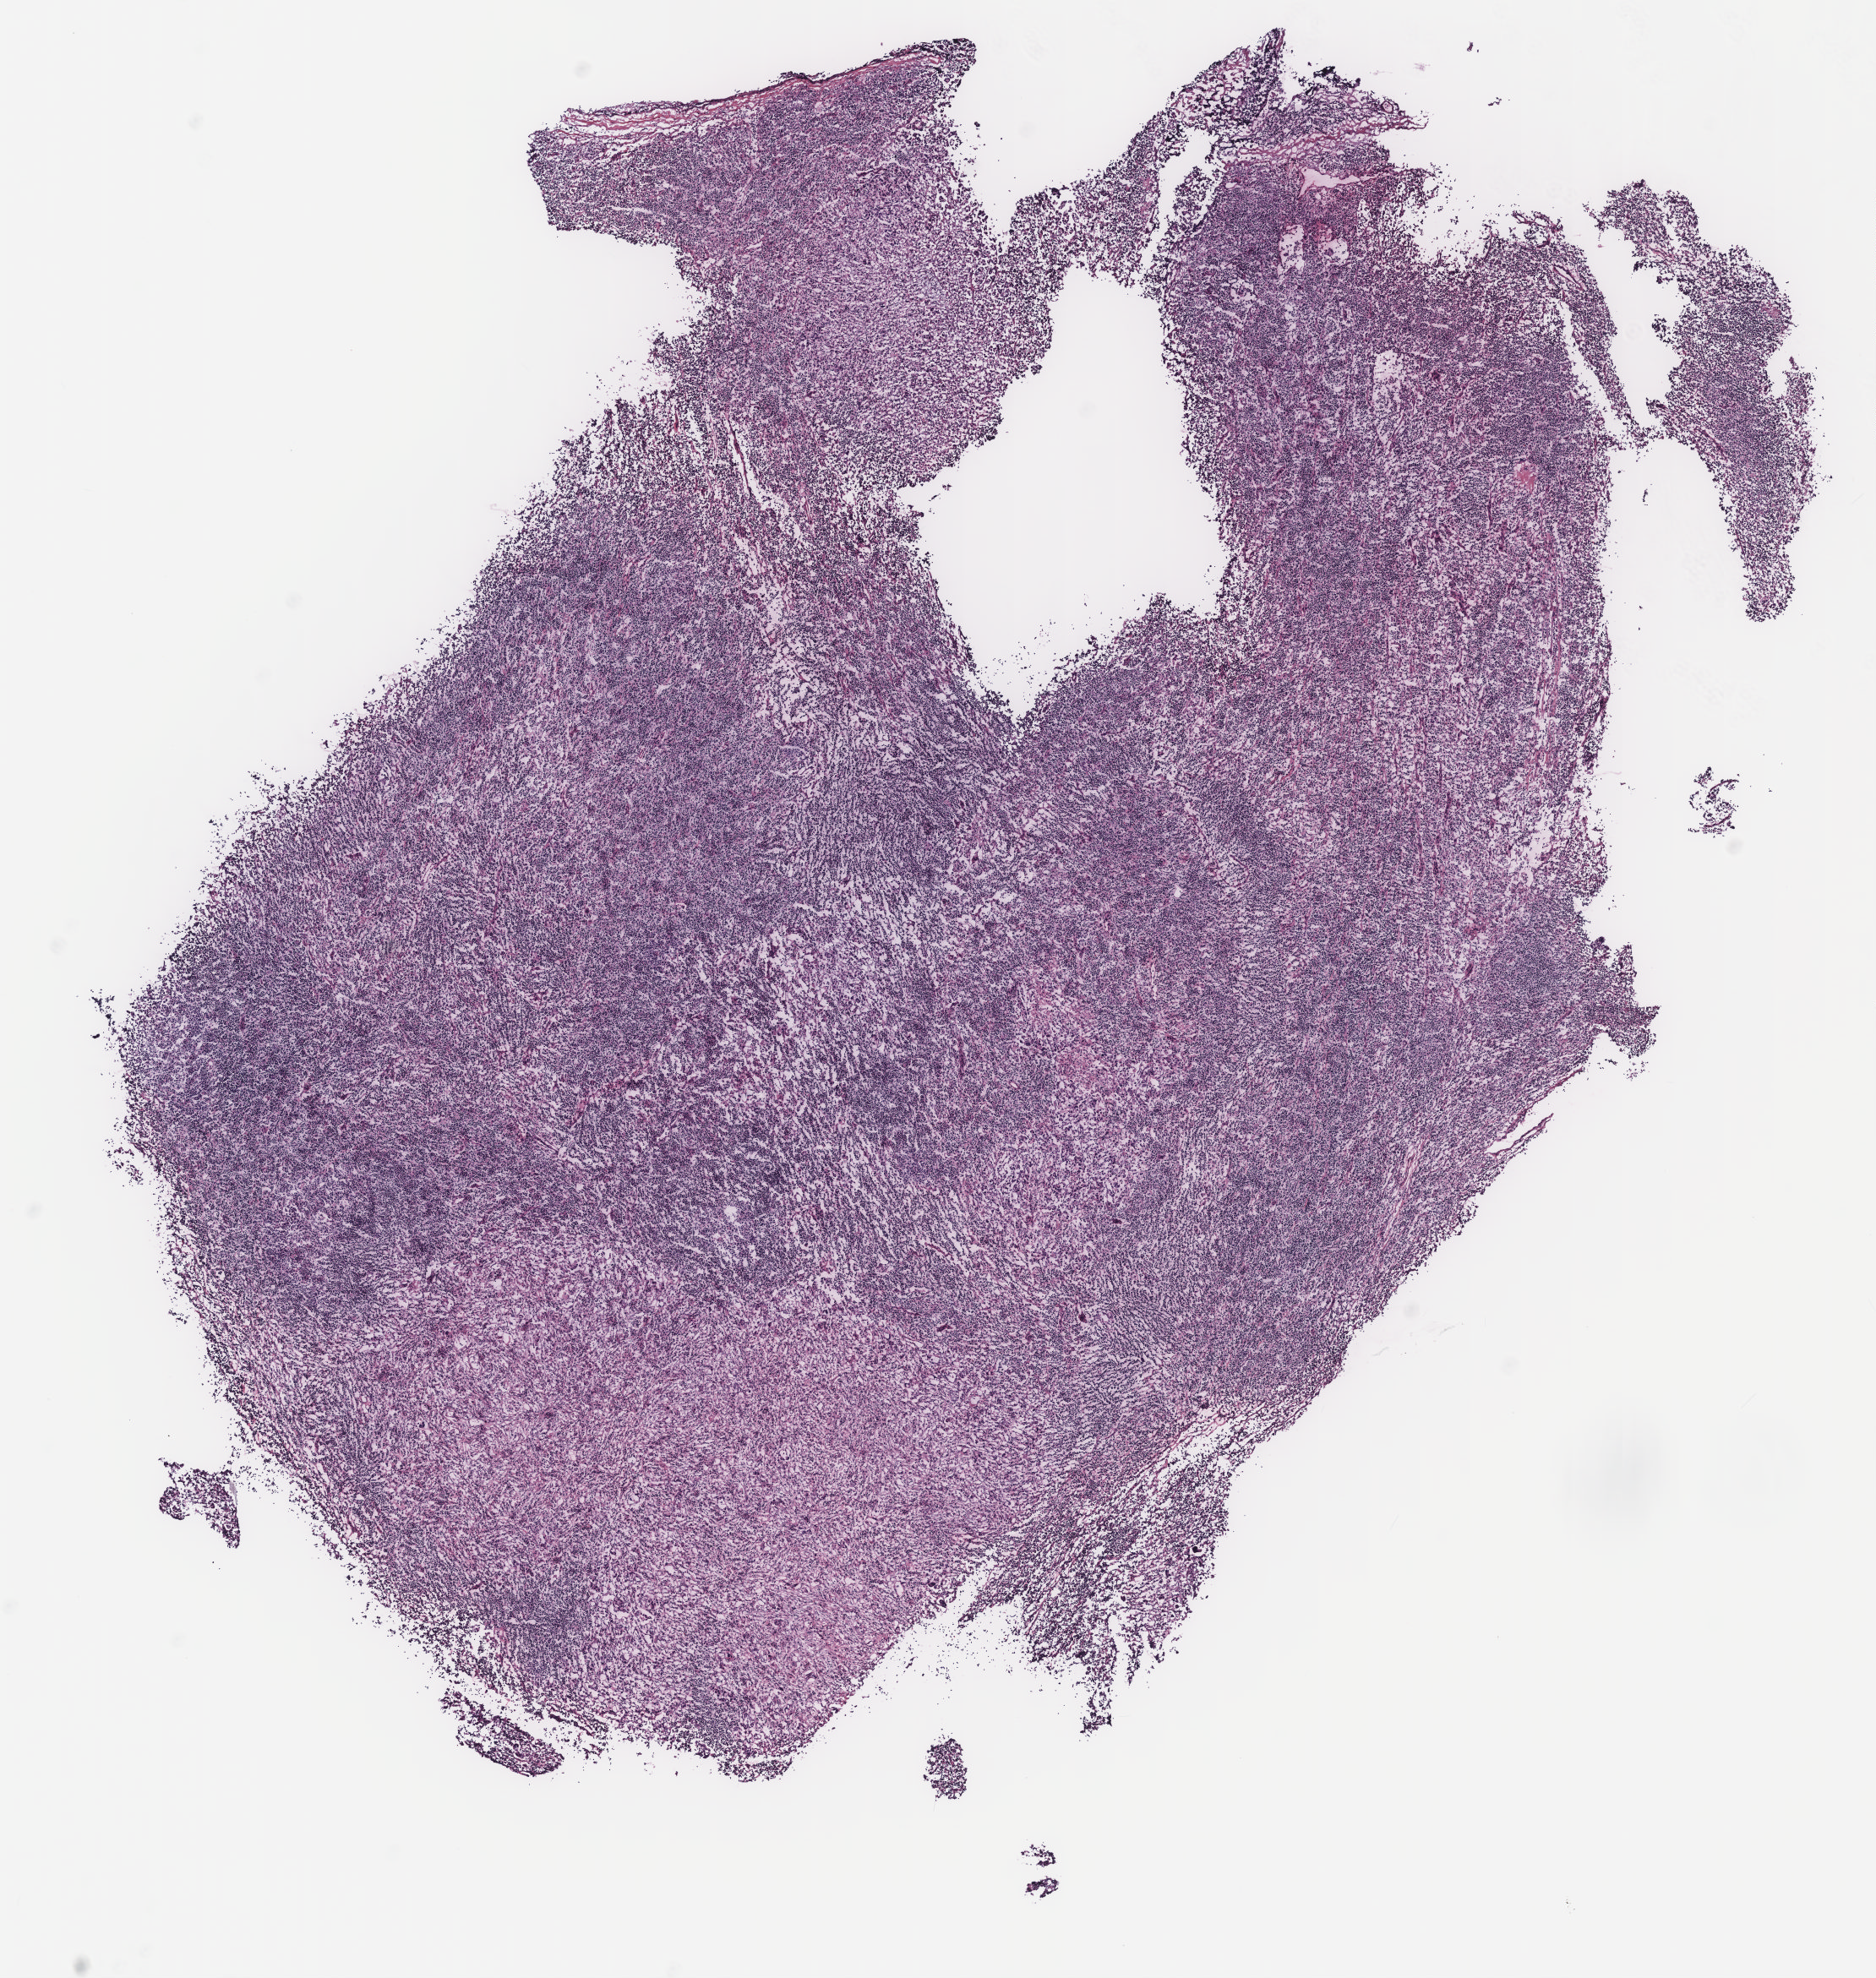
Digitized H&E-stained tissue section (whole slide), a low-resolution overview of the entire scanned area, about 8.9 x 9.4 mm (acquisition: 40x scan); normal (non-tumour) tissue sample, ovary. 48-year-old female patient.
This section: normal (non-tumour) tissue from the same patient. Patient diagnosis: Serous adenocarcinoma, NOS (peritoneum, NOS).